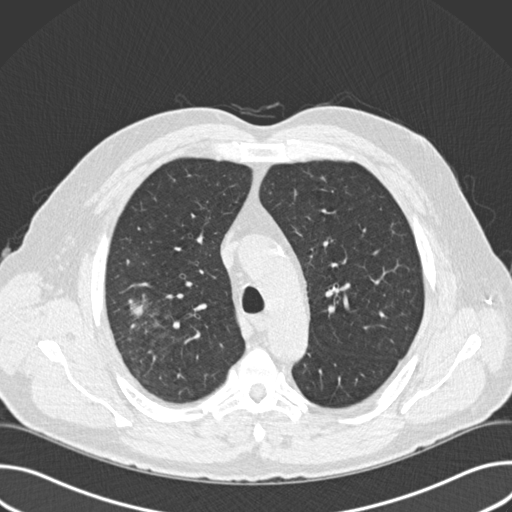
Low-dose screening chest CT, one axial slice; position 117 of 157 along the scan axis; reconstruction kernel B30f; 120 kVp; lung window (W 1500 / L -600 HU); 2 mm slice thickness; 512 × 512 image matrix, field of view 380 × 380 mm.
Annotated regions visible in this slice (outlined manually by an expert reader):
- lesion 1 (tumor, upper lobe of right lung): bounding box (x1, y1, x2, y2) in pixels: (129, 301, 143, 316)